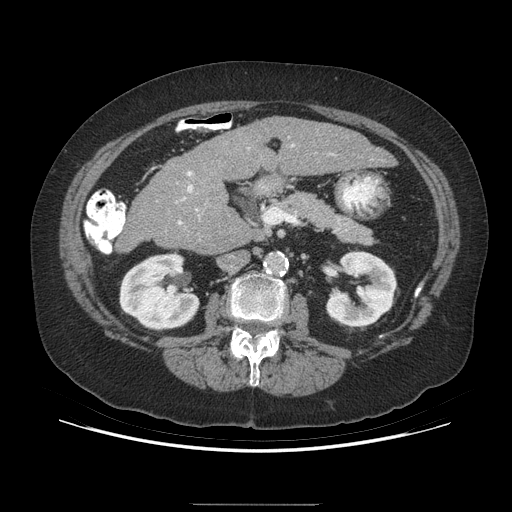
Contrast-enhanced abdominal CT (liver protocol), one axial slice. Slice 140 of 192 in the series (ordered by position). Reconstruction kernel STANDARD. 140 kVp. Soft-tissue window (W 400 / L 40 HU). 2.5 mm slice thickness. 512 × 512 image matrix, field of view 400 × 400 mm. Case-level facts recorded for this patient, not image findings: diagnosis: hepatocellular carcinoma (patient treated with transarterial chemoembolisation; whether this scan precedes or follows treatment is not stated here); TNM stage (as recorded): Stage-I; Child-Pugh class: A; tumour differentiation: moderately differentiated; tumour nodularity: uninodular.
Annotated regions visible in this slice (semi-automatic segmentation, software-assisted and operator-edited):
- liver parenchyma outside the tumour (the mass and vessels are separate outlines, so this box may not span the whole liver): box from (x=194, y=116) to (x=395, y=194) px
- liver vessels: (x=292, y=144)–(x=294, y=147)